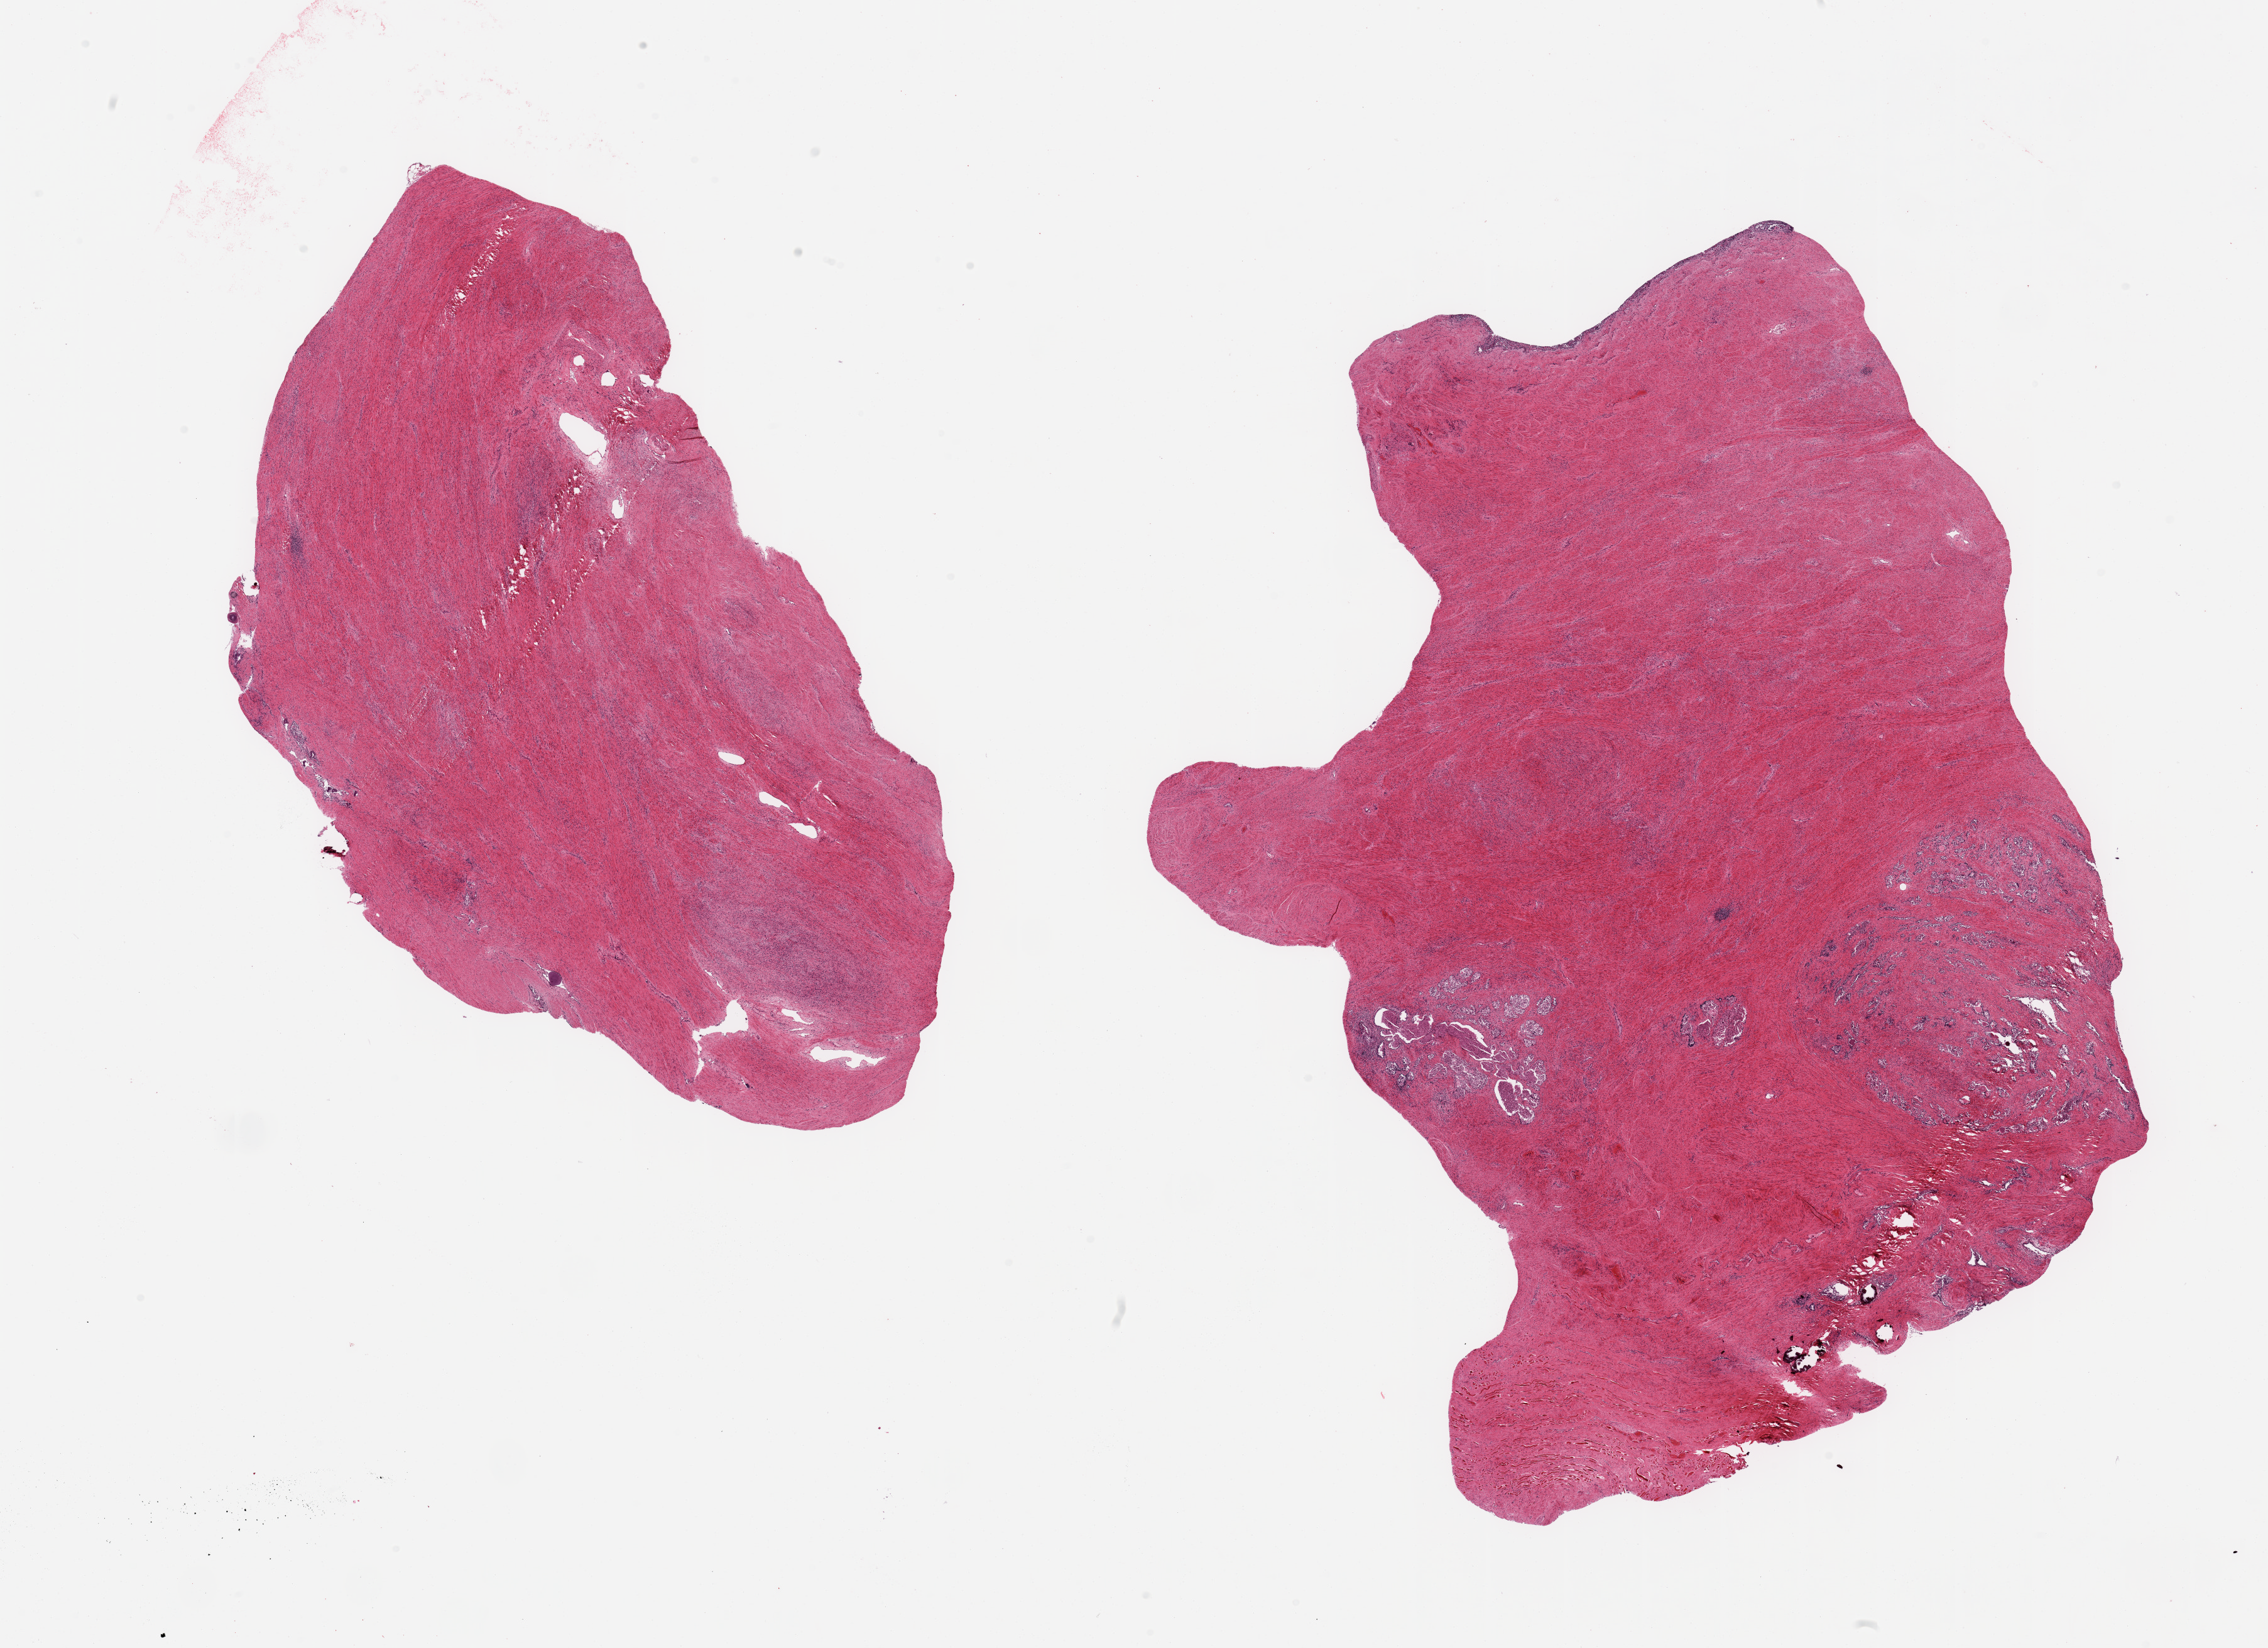
H&E whole-slide image, brightfield, low-resolution overview of the scanned area, about 28.5 x 20.7 mm; PAXgene-fixed paraffin-embedded (PFPE) section; section of prostate (target tissue); donor tissue sample. Male donor.
* review note (as recorded): 2 pieces; predominantly fibromuscular stroma; moderaltly to severely autolyzed glandular component and numerous corpora amylacea; urothelial epithelium